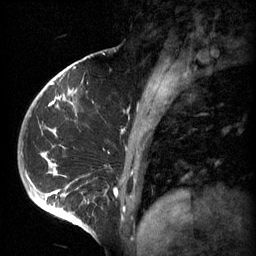
Breast MRI (dynamic contrast-enhanced), one sagittal slice. Slice 20 of 60 in the series (ordered by position). 3 images stored at this slice position (order not interpretable as contrast timing). 1.5 T. TE 4.2 ms, TR 11 ms. 2 mm slice thickness. 256 × 256 image matrix, field of view 200 × 200 mm. Female patient, age 51 years.
Annotated regions visible in this slice (semi-automatic segmentation, software-assisted and operator-edited):
- analysis volume of interest (the breast-tissue region the enhancement analysis was run in; not a lesion): bounding box [x1, y1, x2, y2] px = [48, 82, 161, 197]
- tumour enhancement mask (voxels above the 70 % enhancement threshold inside the analysis volume of interest): [48, 82, 160, 197]